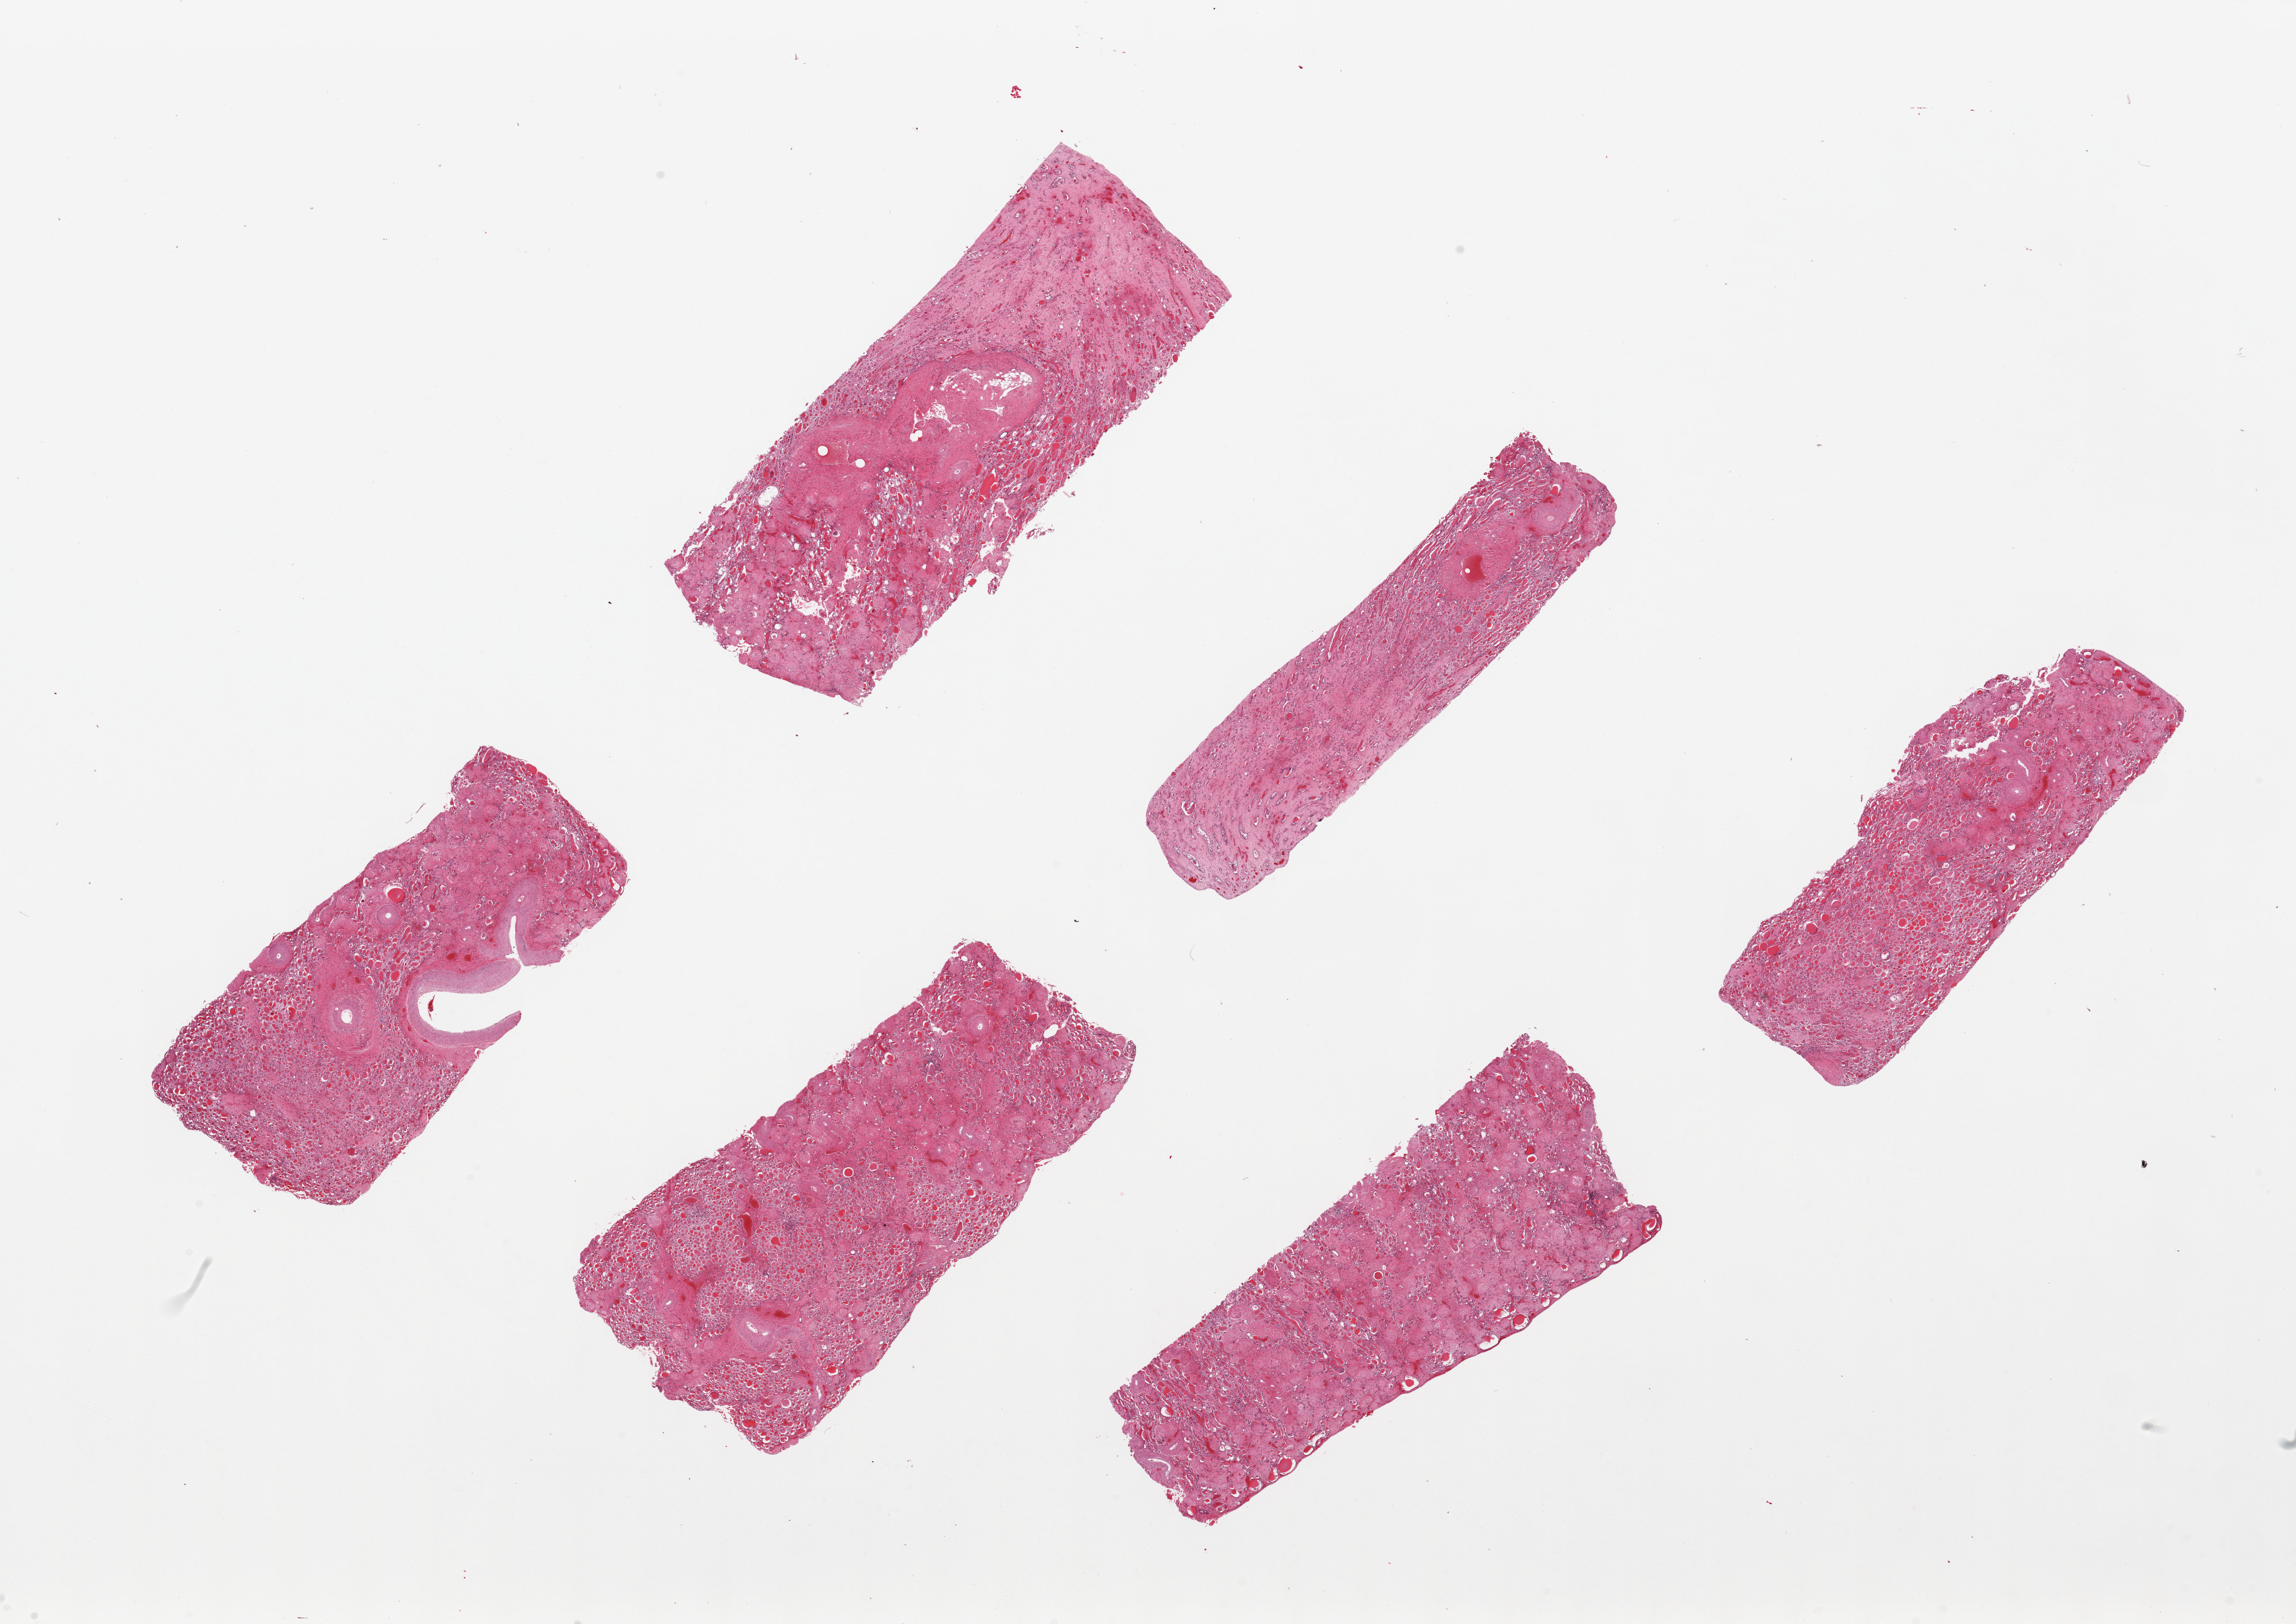
Whole-slide image, haematoxylin and eosin stain — shown as a low-resolution overview of the whole scanned area (about 31.5 x 22.3 mm); PAXgene-fixed paraffin-embedded (PFPE) section; section of renal cortex (target tissue); donor tissue sample. Male donor.
Pathologist's review note for this sample: 6 pieces; end stage kidney with diffuse thyroidization.